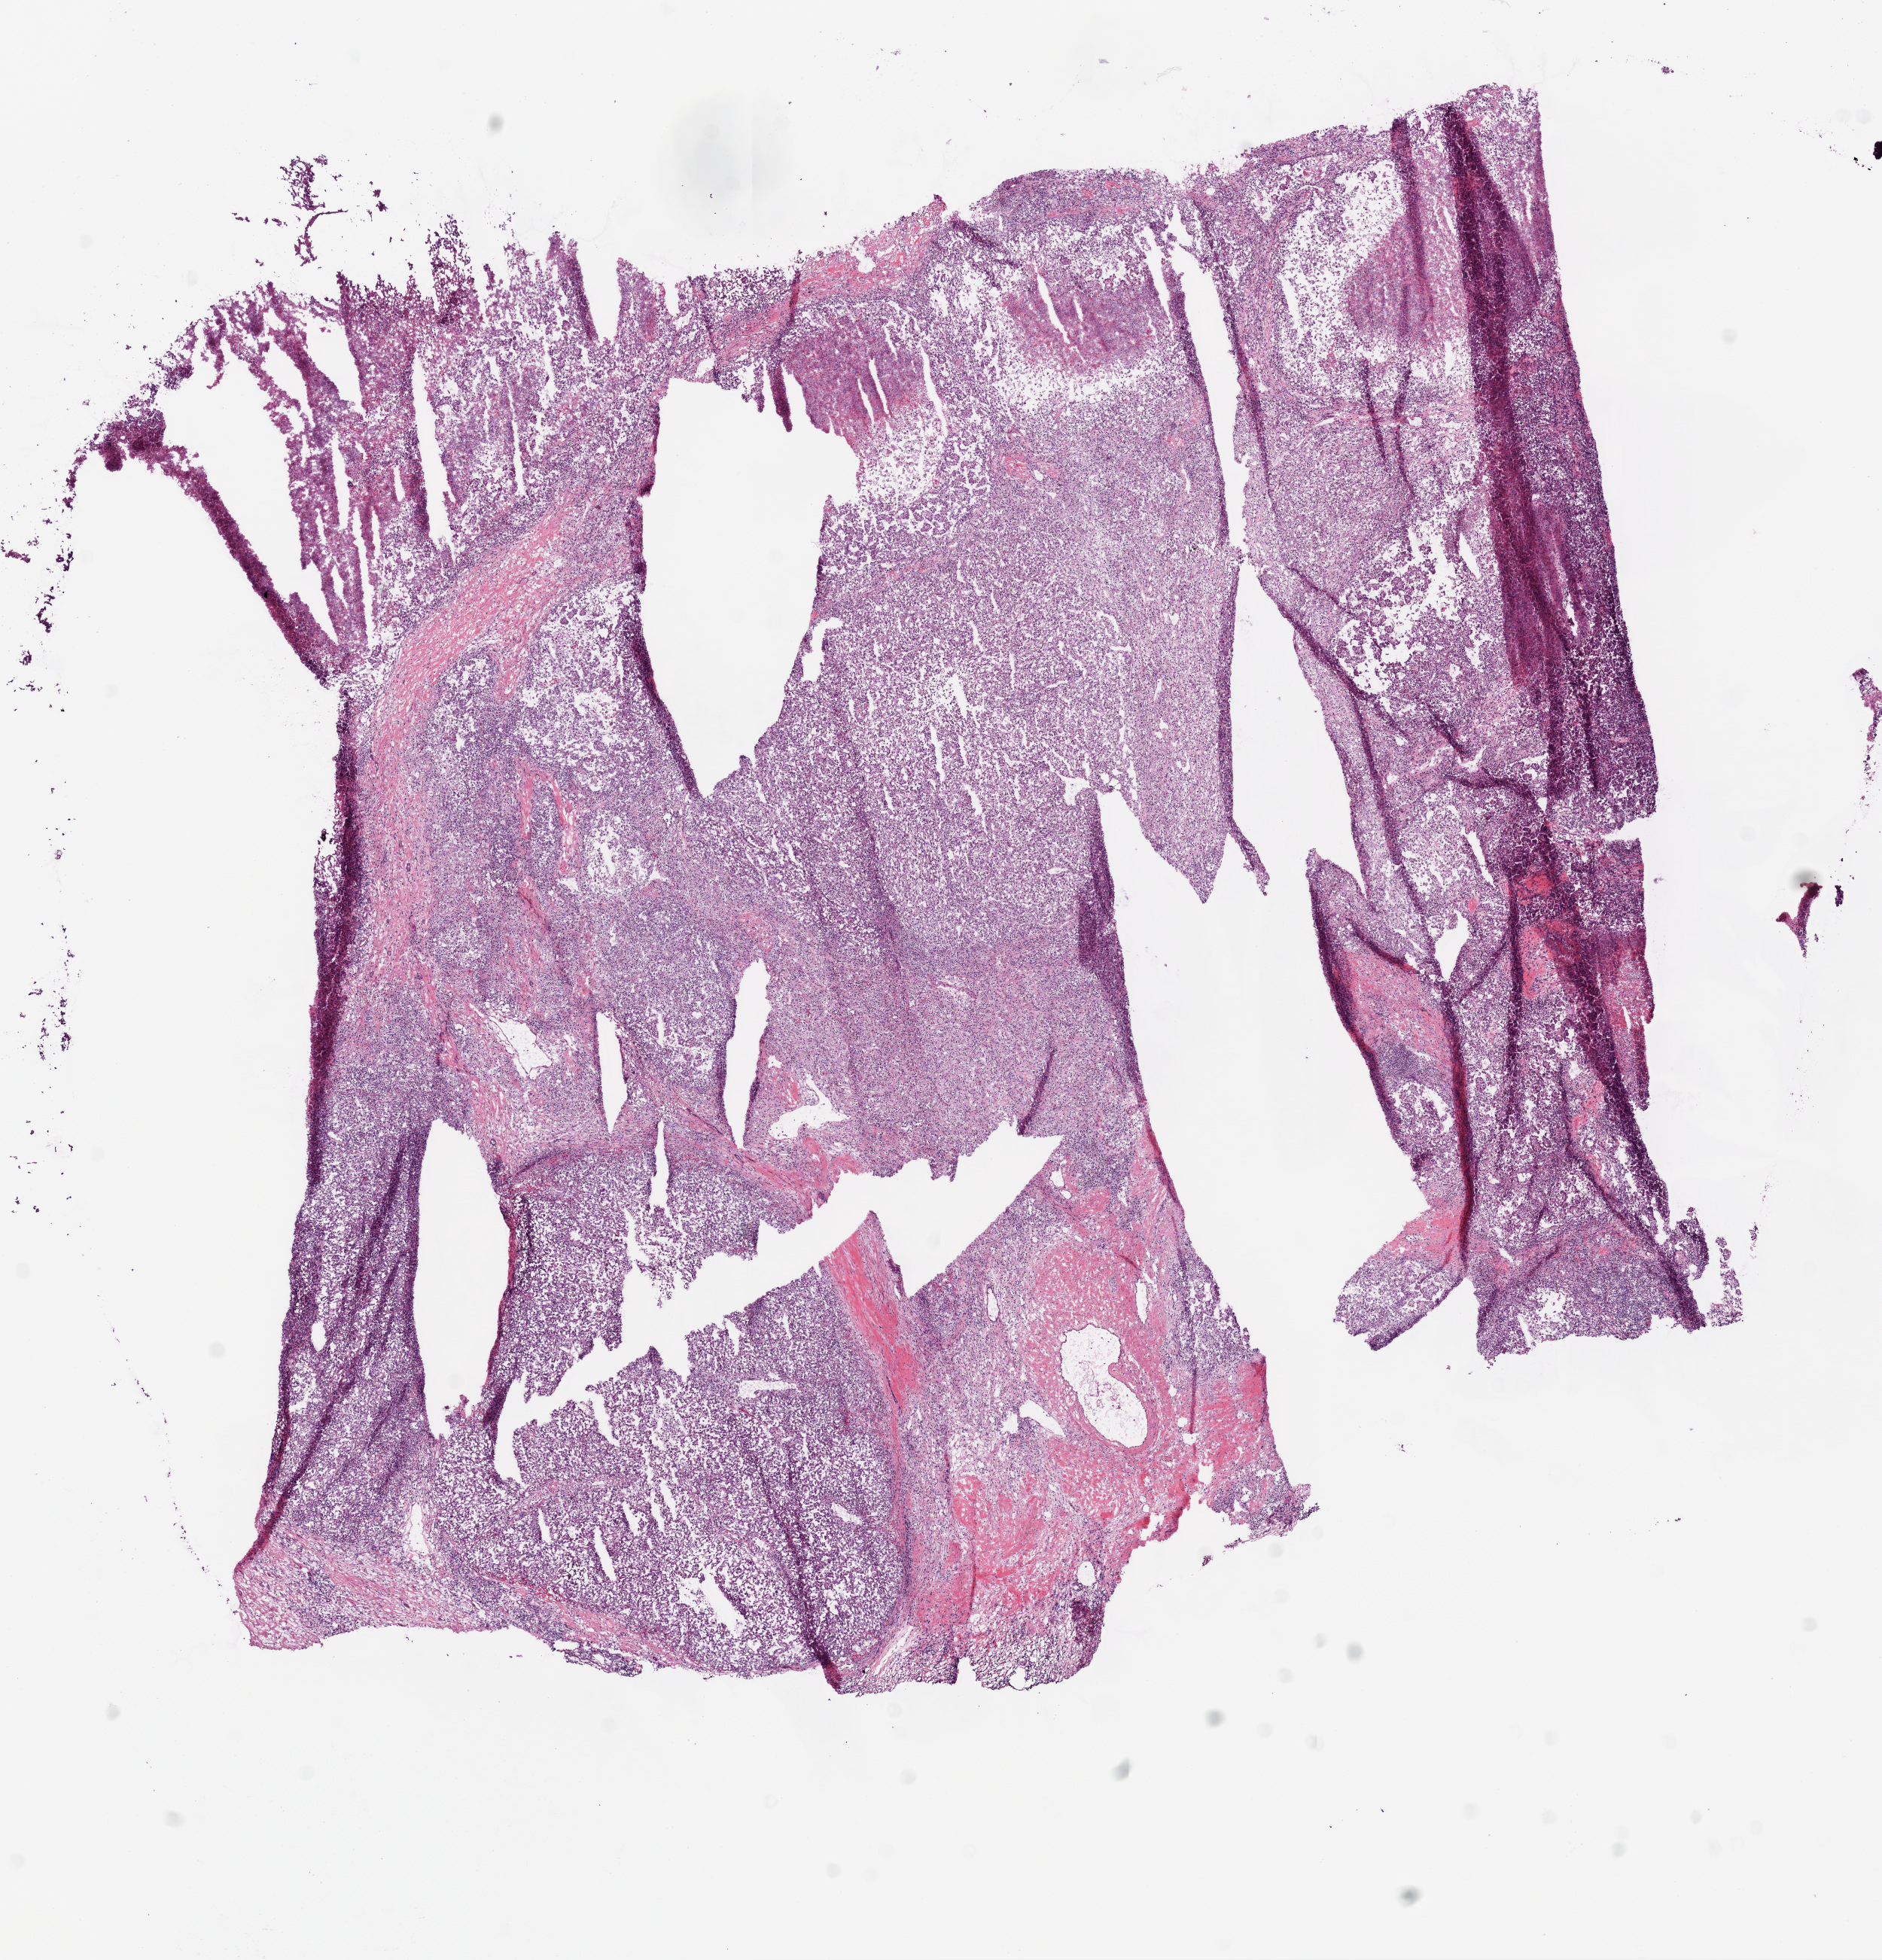
Digitized H&E-stained tissue section (whole slide), low-resolution overview of the scanned area, about 10.0 x 10.4 mm (from a 20x scan). Frozen section. Primary tumour sample from the kidney. Male patient; age at initial diagnosis 37 years. Composition of this section per pathologist review: tumour cells 80%, tumour nuclei 75%.
Pathologic diagnosis: Clear cell adenocarcinoma, NOS.